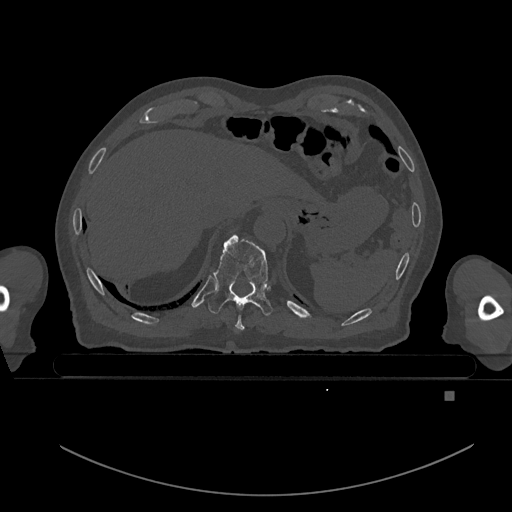
CT including the spine, one axial slice. Position 95 of 969 along the scan axis. Bone window (W 1800 / L 400 HU). 0.5 mm slice thickness. 512 × 512 image matrix, field of view 456 × 456 mm. Male patient, age 82 years. Case-level facts recorded for this patient, not image findings: primary cancer: prostate.
Annotated regions visible in this slice (semi-automatic segmentation, software-assisted and operator-edited):
- T10 vertebra: bounding box <208,234,273,316> (left, top, right, bottom; pixels)
- T9 vertebra: <235,315,245,331>